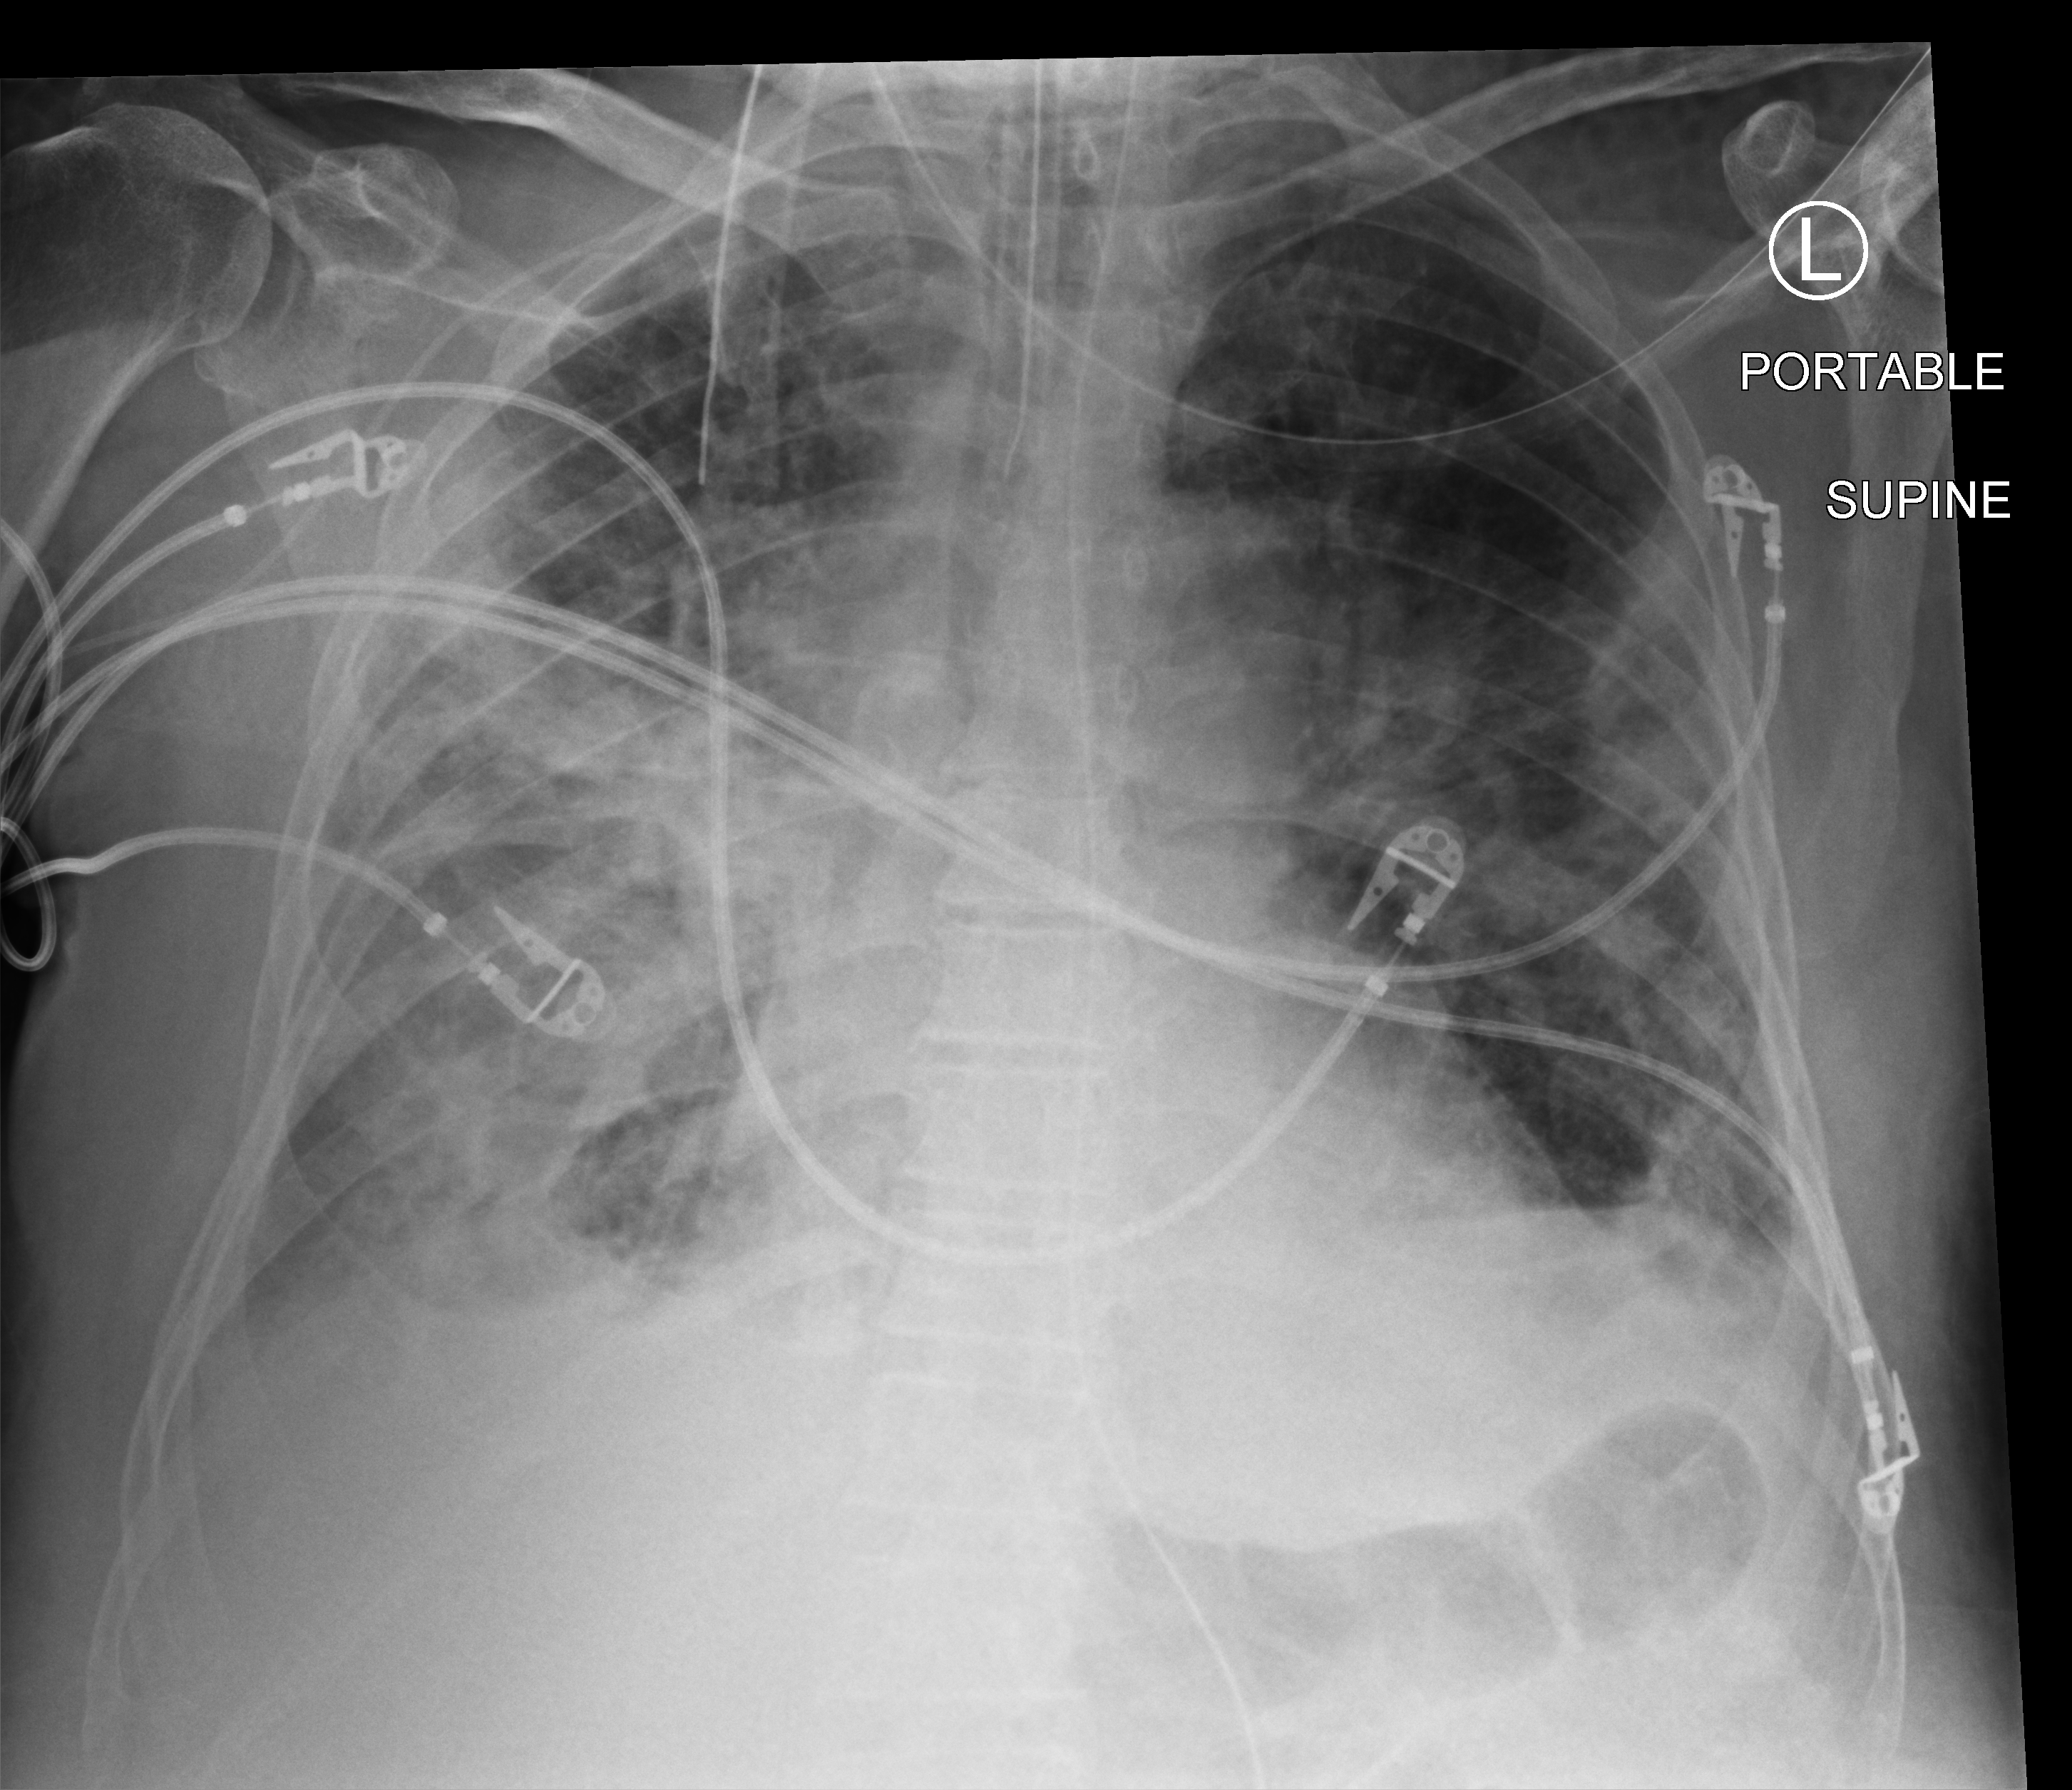
Chest X-ray (portable), anteroposterior (AP) projection. Male patient hospitalised with COVID-19, age 75–90 years.
Admission-level facts for this patient (not findings on this image; timing relative to this image not recorded): other chronic lung disease (admission record): yes.